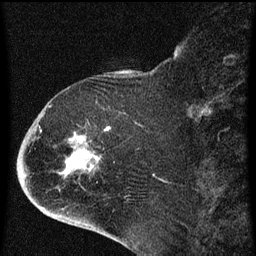
Breast MRI (dynamic contrast-enhanced), one sagittal slice. Position 21 of 60 along the scan axis. Dynamic contrast-enhanced series, image 2 of 4 at this slice position (ordered by acquisition). 1.5 T. TE 4.2 ms, TR 8 ms. 2 mm slice thickness. 256 × 256 image matrix, field of view 180 × 180 mm. Patient: female, 71 years.
Annotated regions visible in this slice (semi-automatically segmented with operator editing):
- analysis volume of interest (the breast-tissue region the enhancement analysis was run in; not a lesion): bounding box <32,86,130,205> (left, top, right, bottom; pixels)
- tumour enhancement mask (voxels above the 70 % enhancement threshold inside the analysis volume of interest): <40,126,110,173>